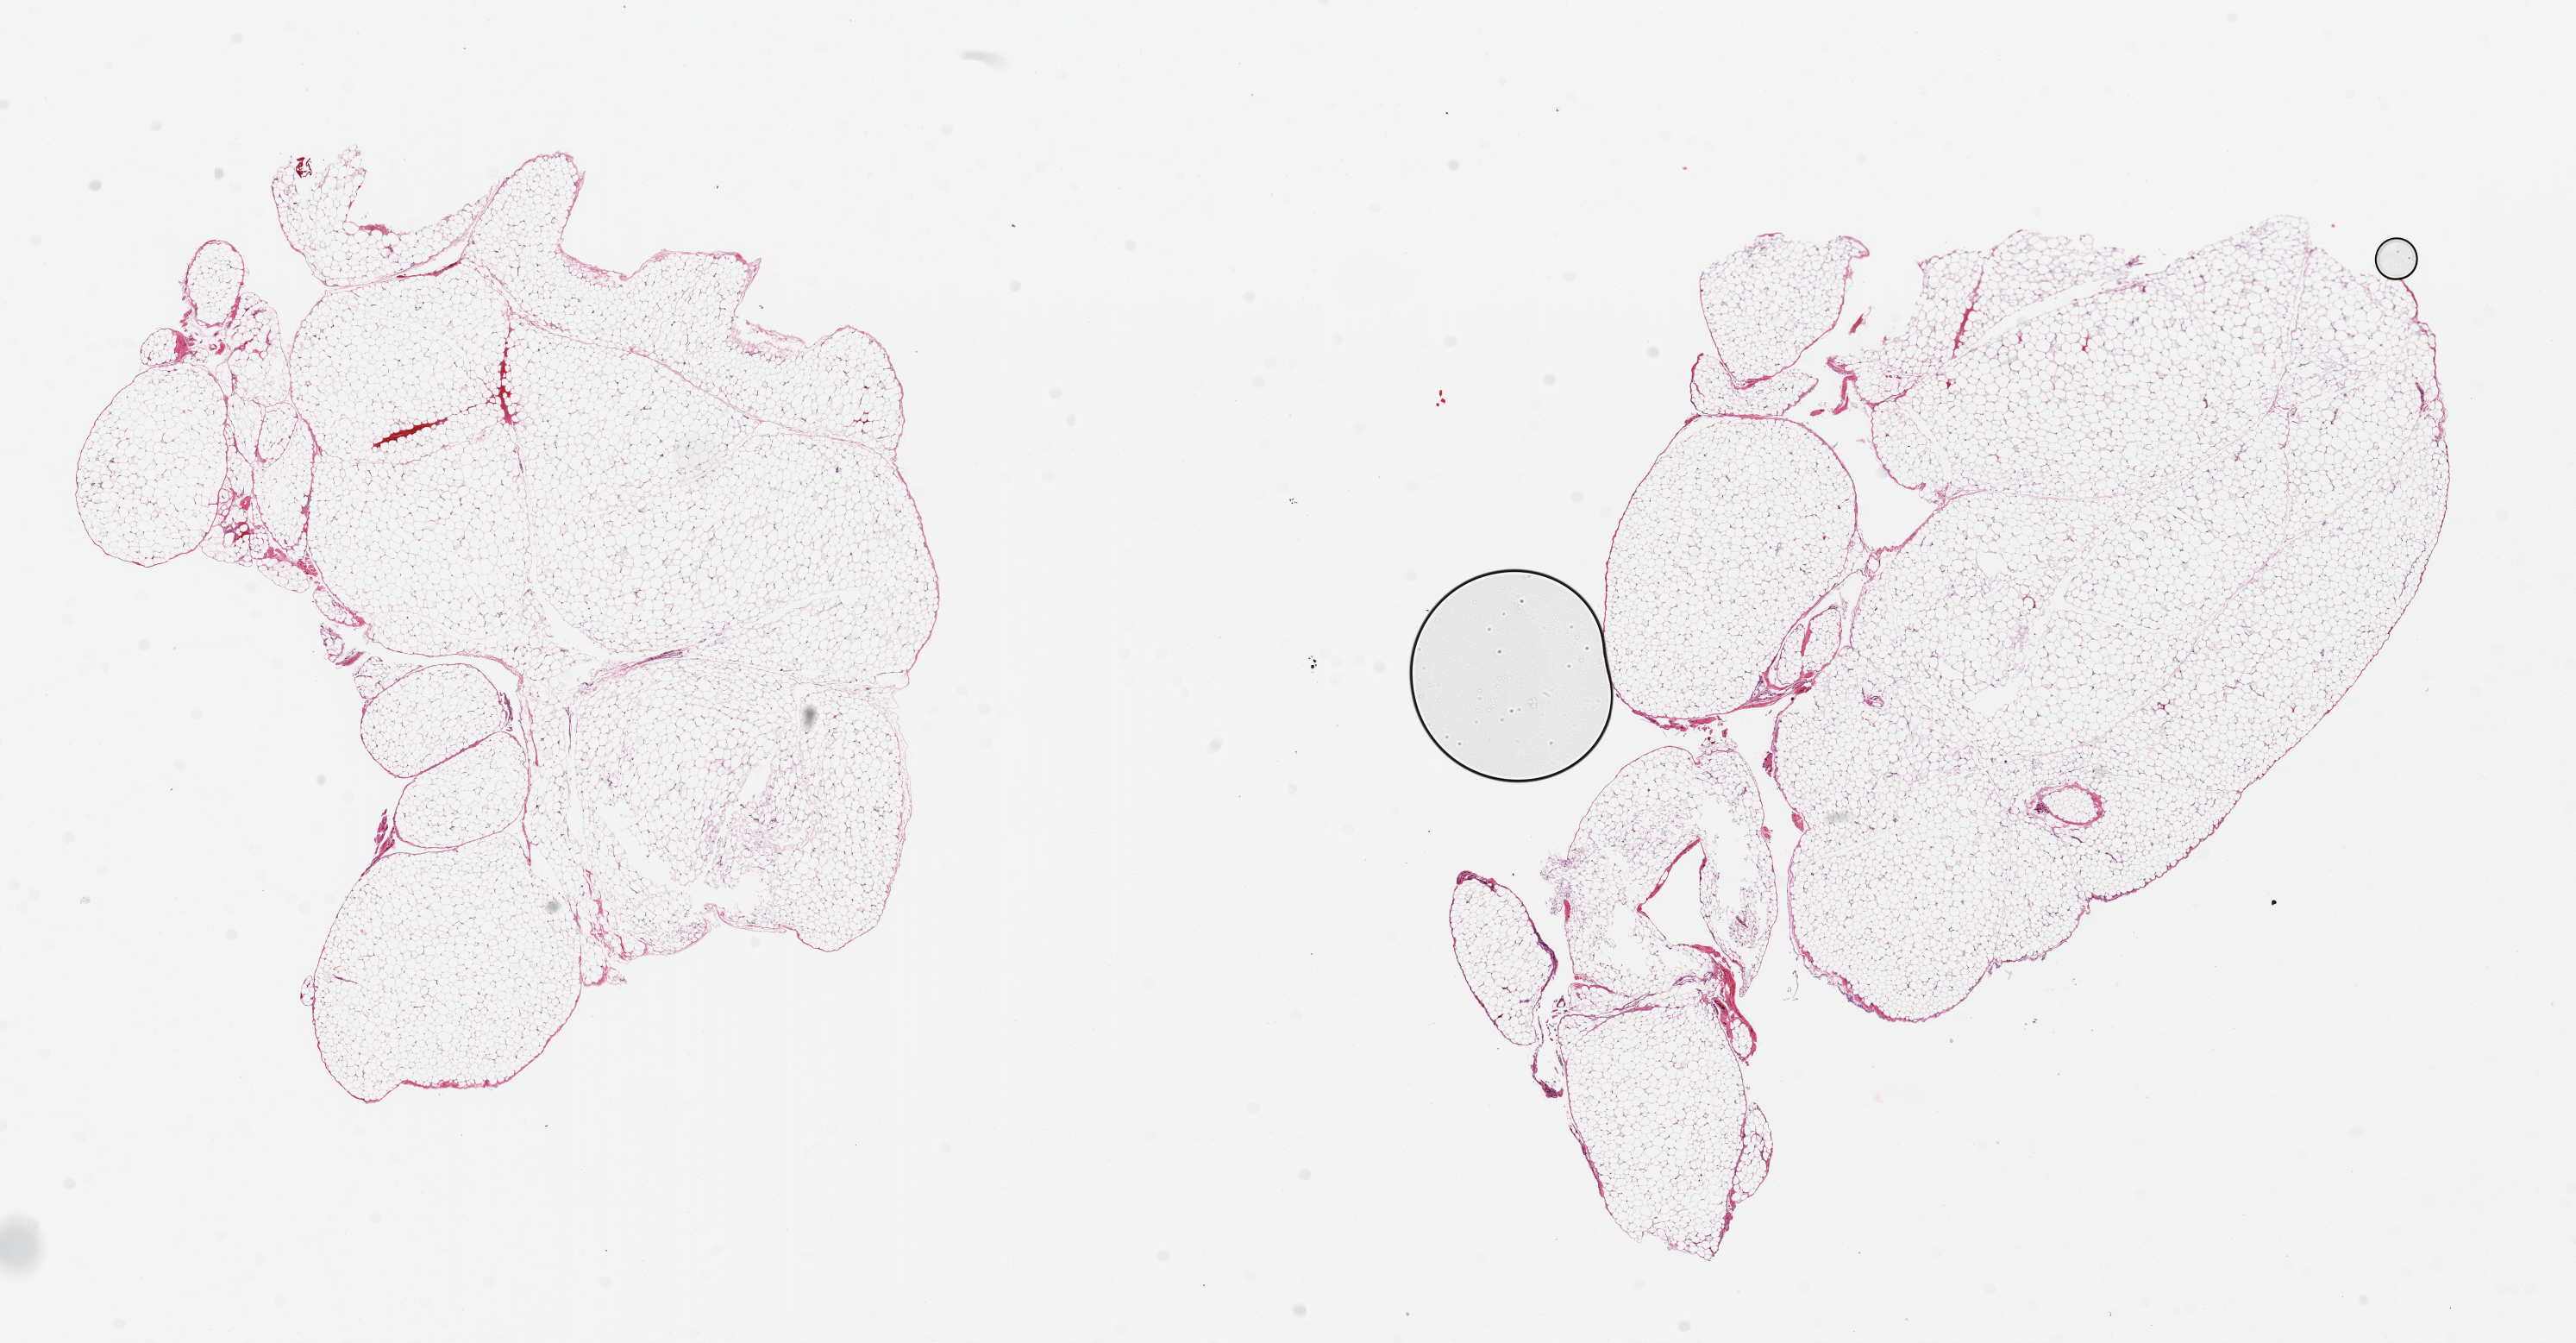
Whole-slide image, haematoxylin and eosin stain, low-resolution overview of the scanned area, about 23.6 x 12.3 mm (acquisition: 20x scan). PAXgene-fixed, paraffin-embedded tissue. Sampled site (target tissue): omentum. Donor tissue sample. Male donor.
Pathologist's review note for this sample: 2 pieces ~9x6mm.